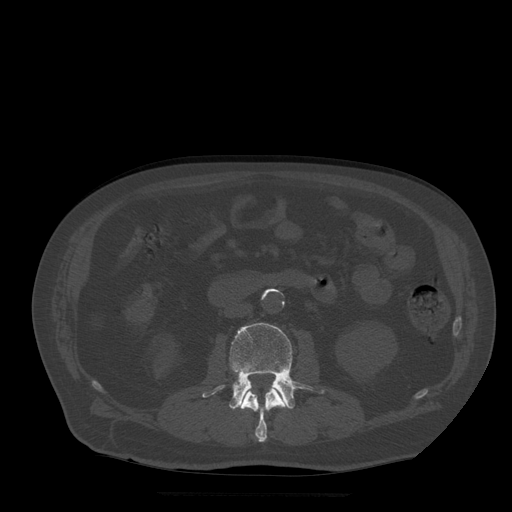
CT including the spine, one axial slice; bone window (W 1800 / L 400 HU); 1.25 mm slice thickness; 512 × 512 image matrix, field of view 420 × 420 mm. Patient age 72 years. From the clinical record (not read from this slice): primary cancer: prostate.
Structures marked on this image (semi-automatically segmented with operator editing):
- L2 vertebra: bounding box [x1, y1, x2, y2] px = [241, 387, 286, 443]
- L3 vertebra: [203, 323, 324, 409]